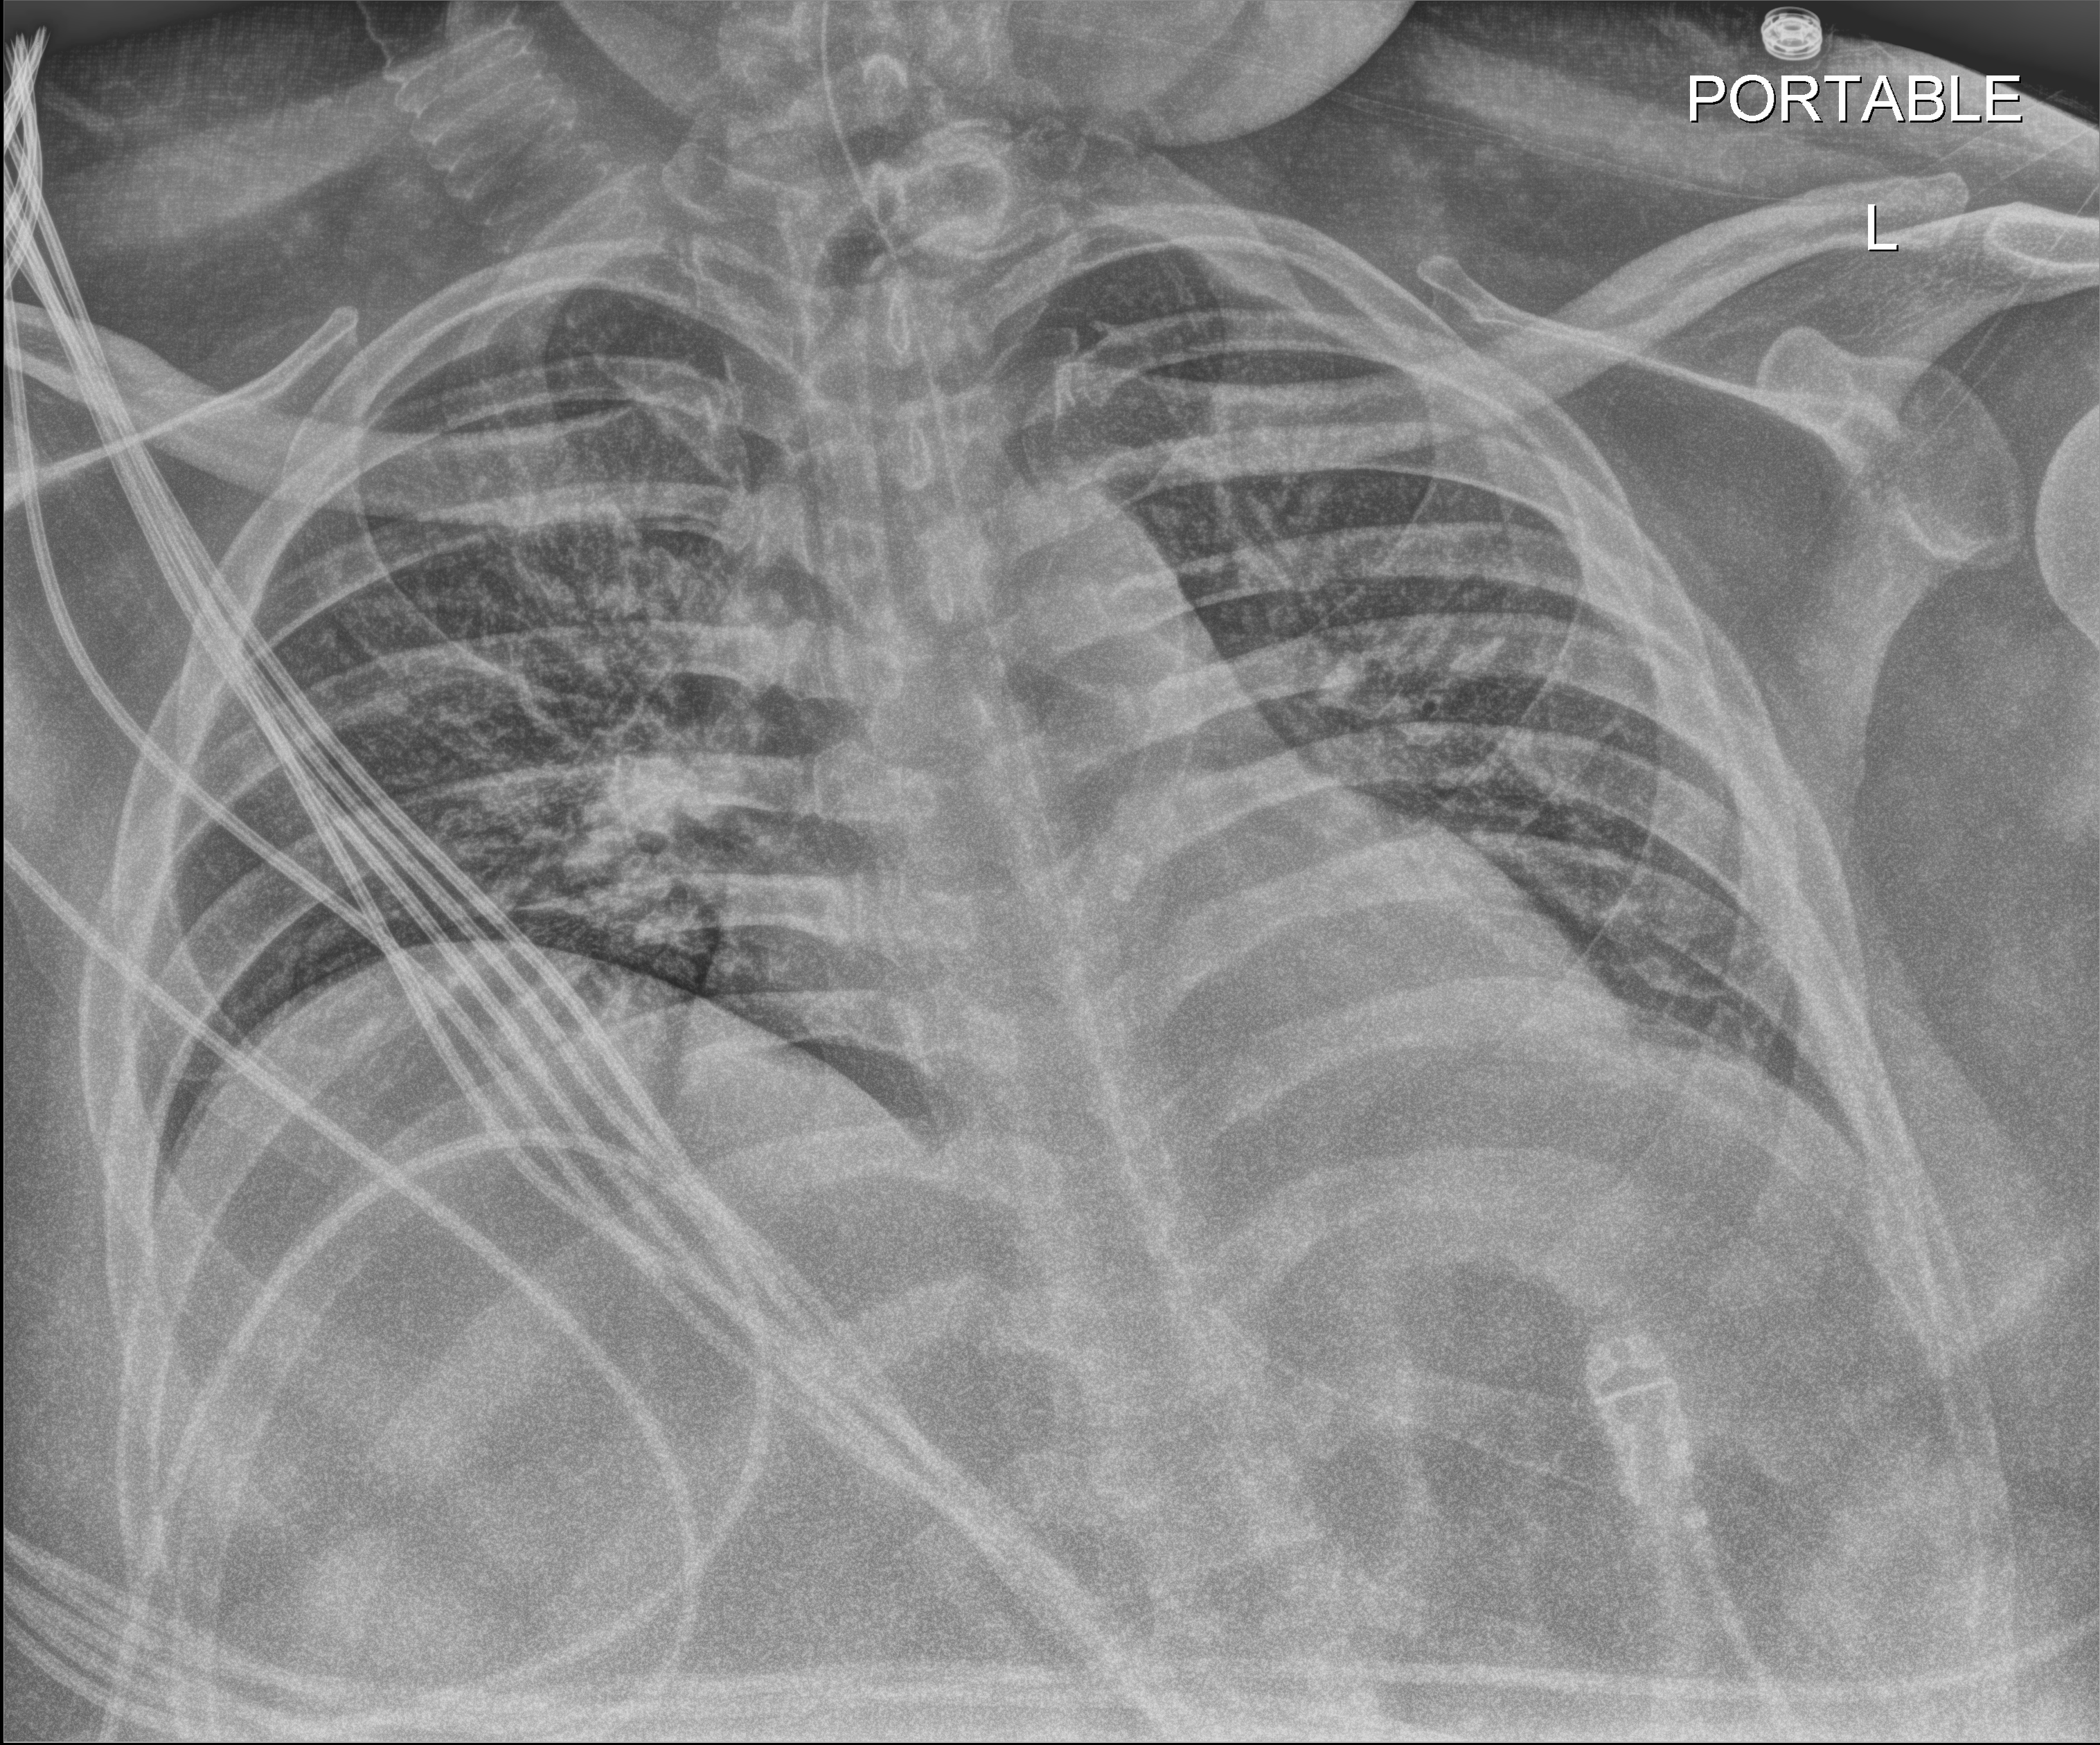
Portable chest radiograph. Male patient hospitalised with COVID-19, age 18–59 years.
Hospital-stay facts (about this admission, not read from this image; timing relative to this image not recorded): admitted to intensive care during this hospital stay: yes; mechanically ventilated during this hospital stay: yes; diabetes (admission record): yes.